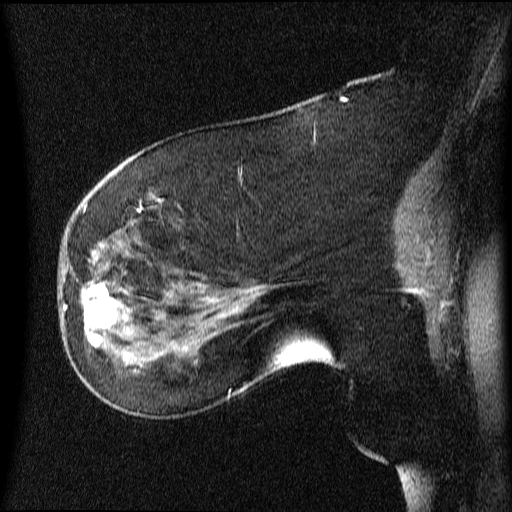
Breast MRI (dynamic contrast-enhanced), one sagittal slice; position 26 of 64 along the scan axis; dynamic contrast-enhanced series, image 2 of 4 at this slice position (ordered by acquisition); 1.5 T; TE 4.2 ms, TR 9 ms; 2 mm slice thickness; 512 × 512 image matrix, field of view 200 × 200 mm. Female patient, age 63 years.
Outlined on this slice (semi-automatic segmentation, software-assisted and operator-edited):
- analysis volume of interest (the breast-tissue region the enhancement analysis was run in; not a lesion): bounding box [x1, y1, x2, y2] px = [66, 272, 131, 353]
- tumour enhancement mask (voxels above the 70 % enhancement threshold inside the analysis volume of interest): [85, 284, 119, 349]